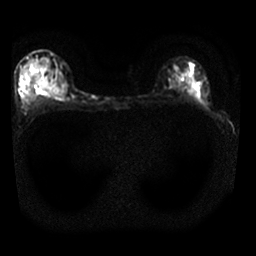
Breast MRI, one axial slice. Position 18 of 25 along the scan axis. Diffusion-weighted series; image 2 of 4 stored at this slice position (different b-values; order by instance number). 1.5 T. 256 × 256 image matrix, field of view 310 × 310 mm. Female patient.
Outlined on this slice (outlined manually by an expert reader):
- tumour on diffusion-weighted imaging: bounding box (x1, y1, x2, y2) in pixels: (40, 86, 44, 90)